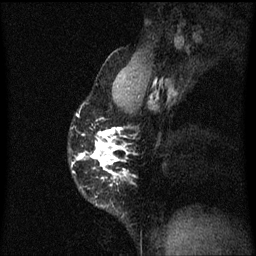
Breast MRI (dynamic contrast-enhanced), one sagittal slice. Slice 43 of 60 in the series (ordered by position). Dynamic contrast-enhanced series, image 2 of 3 at this slice position (ordered by acquisition). 1.5 T. TE 4.2 ms, TR 8.4 ms. 2 mm slice thickness. 256 × 256 image matrix, field of view 200 × 200 mm. Patient: female, 40 years.
Outlined on this slice (semi-automatic segmentation, software-assisted and operator-edited):
- analysis volume of interest (the breast-tissue region the enhancement analysis was run in; not a lesion): bounding box (x1, y1, x2, y2) in pixels: (71, 110, 128, 211)
- tumour enhancement mask (voxels above the 70 % enhancement threshold inside the analysis volume of interest): (74, 114, 124, 175)